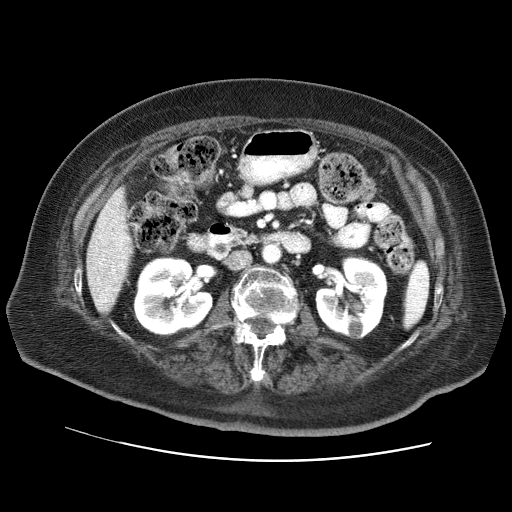
Contrast-enhanced abdominal CT (liver protocol), one axial slice. Position 22 of 73 along the scan axis. Reconstruction kernel STANDARD. Soft-tissue window (W 400 / L 40 HU). 2.5 mm slice thickness. 512 × 512 image matrix, field of view 380 × 380 mm. From the clinical record (not read from this slice): diagnosis: hepatocellular carcinoma (patient treated with transarterial chemoembolisation; whether this scan precedes or follows treatment is not stated here); TNM stage (as recorded): Stage-I.
Structures marked on this image (semi-automatically segmented with operator editing):
- liver parenchyma outside the tumour (the mass and vessels are separate outlines, so this box may not span the whole liver): box from (x=86, y=188) to (x=132, y=312) px
- liver vessels: (x=96, y=221)–(x=128, y=303)